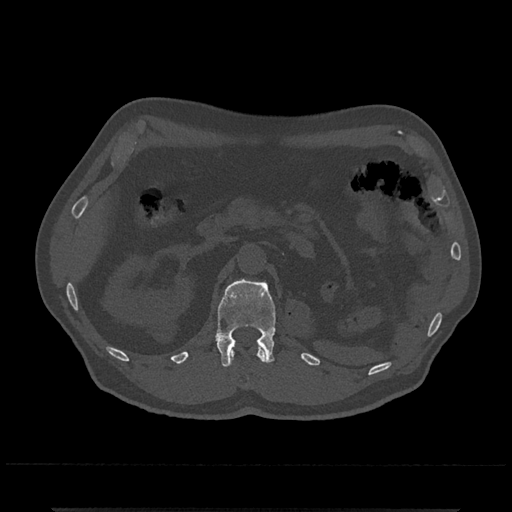
CT including the spine, one axial slice; position 378 of 797 along the scan axis; reconstruction kernel Br40s/3; bone window (W 1800 / L 400 HU); 512 × 512 image matrix, field of view 393 × 393 mm. Male patient, age 67 years. From the clinical record (not read from this slice): primary cancer: prostate.
Structures marked on this image (semi-automatically segmented with operator editing):
- L1 vertebra: bounding box <214,278,276,367> (left, top, right, bottom; pixels)
- T12 vertebra: <230,346,266,363>